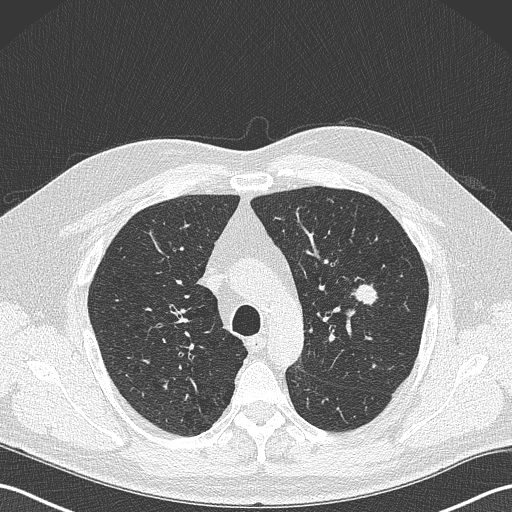
Chest CT (low-dose screening protocol), one axial image, baseline annual screen, lung window (W 1500 / L -600 HU), 1 mm slice thickness, lung (sharp) reconstruction kernel (B50f), slice 98 of 343 in the series, 512 × 512 image matrix. Male, age 61 years at enrolment. Former smoker at enrolment.
- Expert-annotated lung lesion, bounding box (x1, y1, x2, y2) in pixels: (342, 276, 385, 316).
- The screening reader recorded 2 non-calcified nodules or masses ≥4 mm on this exam; which of them this box marks is not recorded.
- Official screen result: positive, change unspecified: nodule(s) >= 4 mm or enlarging nodule(s), mass(es), or other non-specific abnormalities suspicious for lung cancer.
- Later outcome: lung cancer diagnosed 160 days after this screen — adenocarcinoma, NOS, left upper lobe, poorly differentiated (G3), stage IA (AJCC 6th edition), 28 mm at pathology.